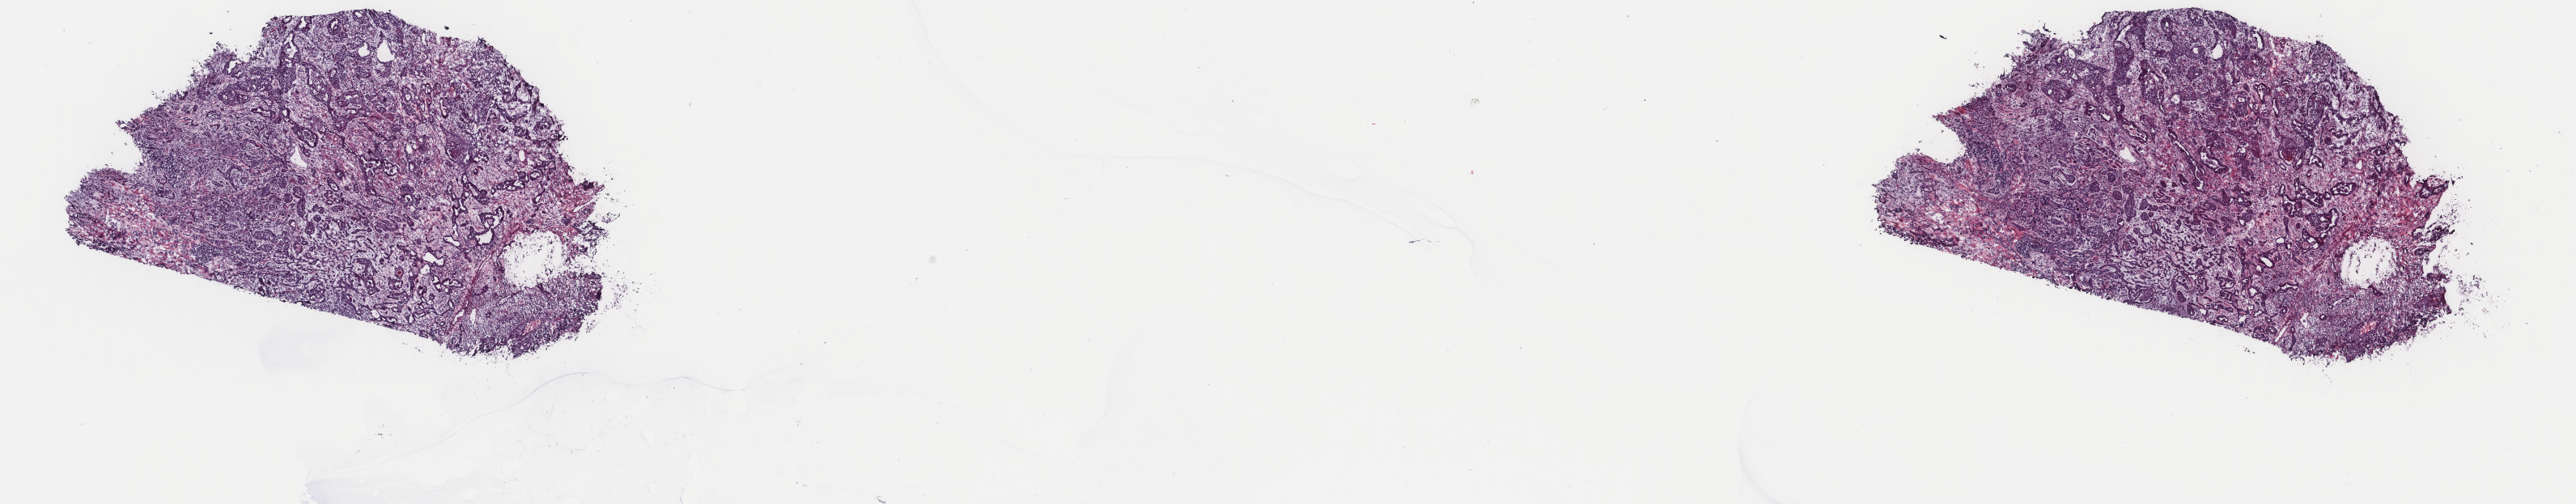
H&E-stained whole-slide image — whole scanned area (about 25.3 x 4.9 mm, from a 40x scan) shown as a low-resolution overview. Frozen section. Uterus, primary tumour sample. Female, age 84 years at initial diagnosis. Composition of this section per pathologist review: tumour cells 85%, tumour nuclei 90%, normal cells 0%, stromal cells 15%, necrosis 0%. Infiltration values recorded for this section: lymphocyte infiltration 0%, monocyte infiltration 0%, neutrophil infiltration 0%.
FIGO stage: IIIC. Pathologic diagnosis: Mullerian mixed tumor (endometrium).